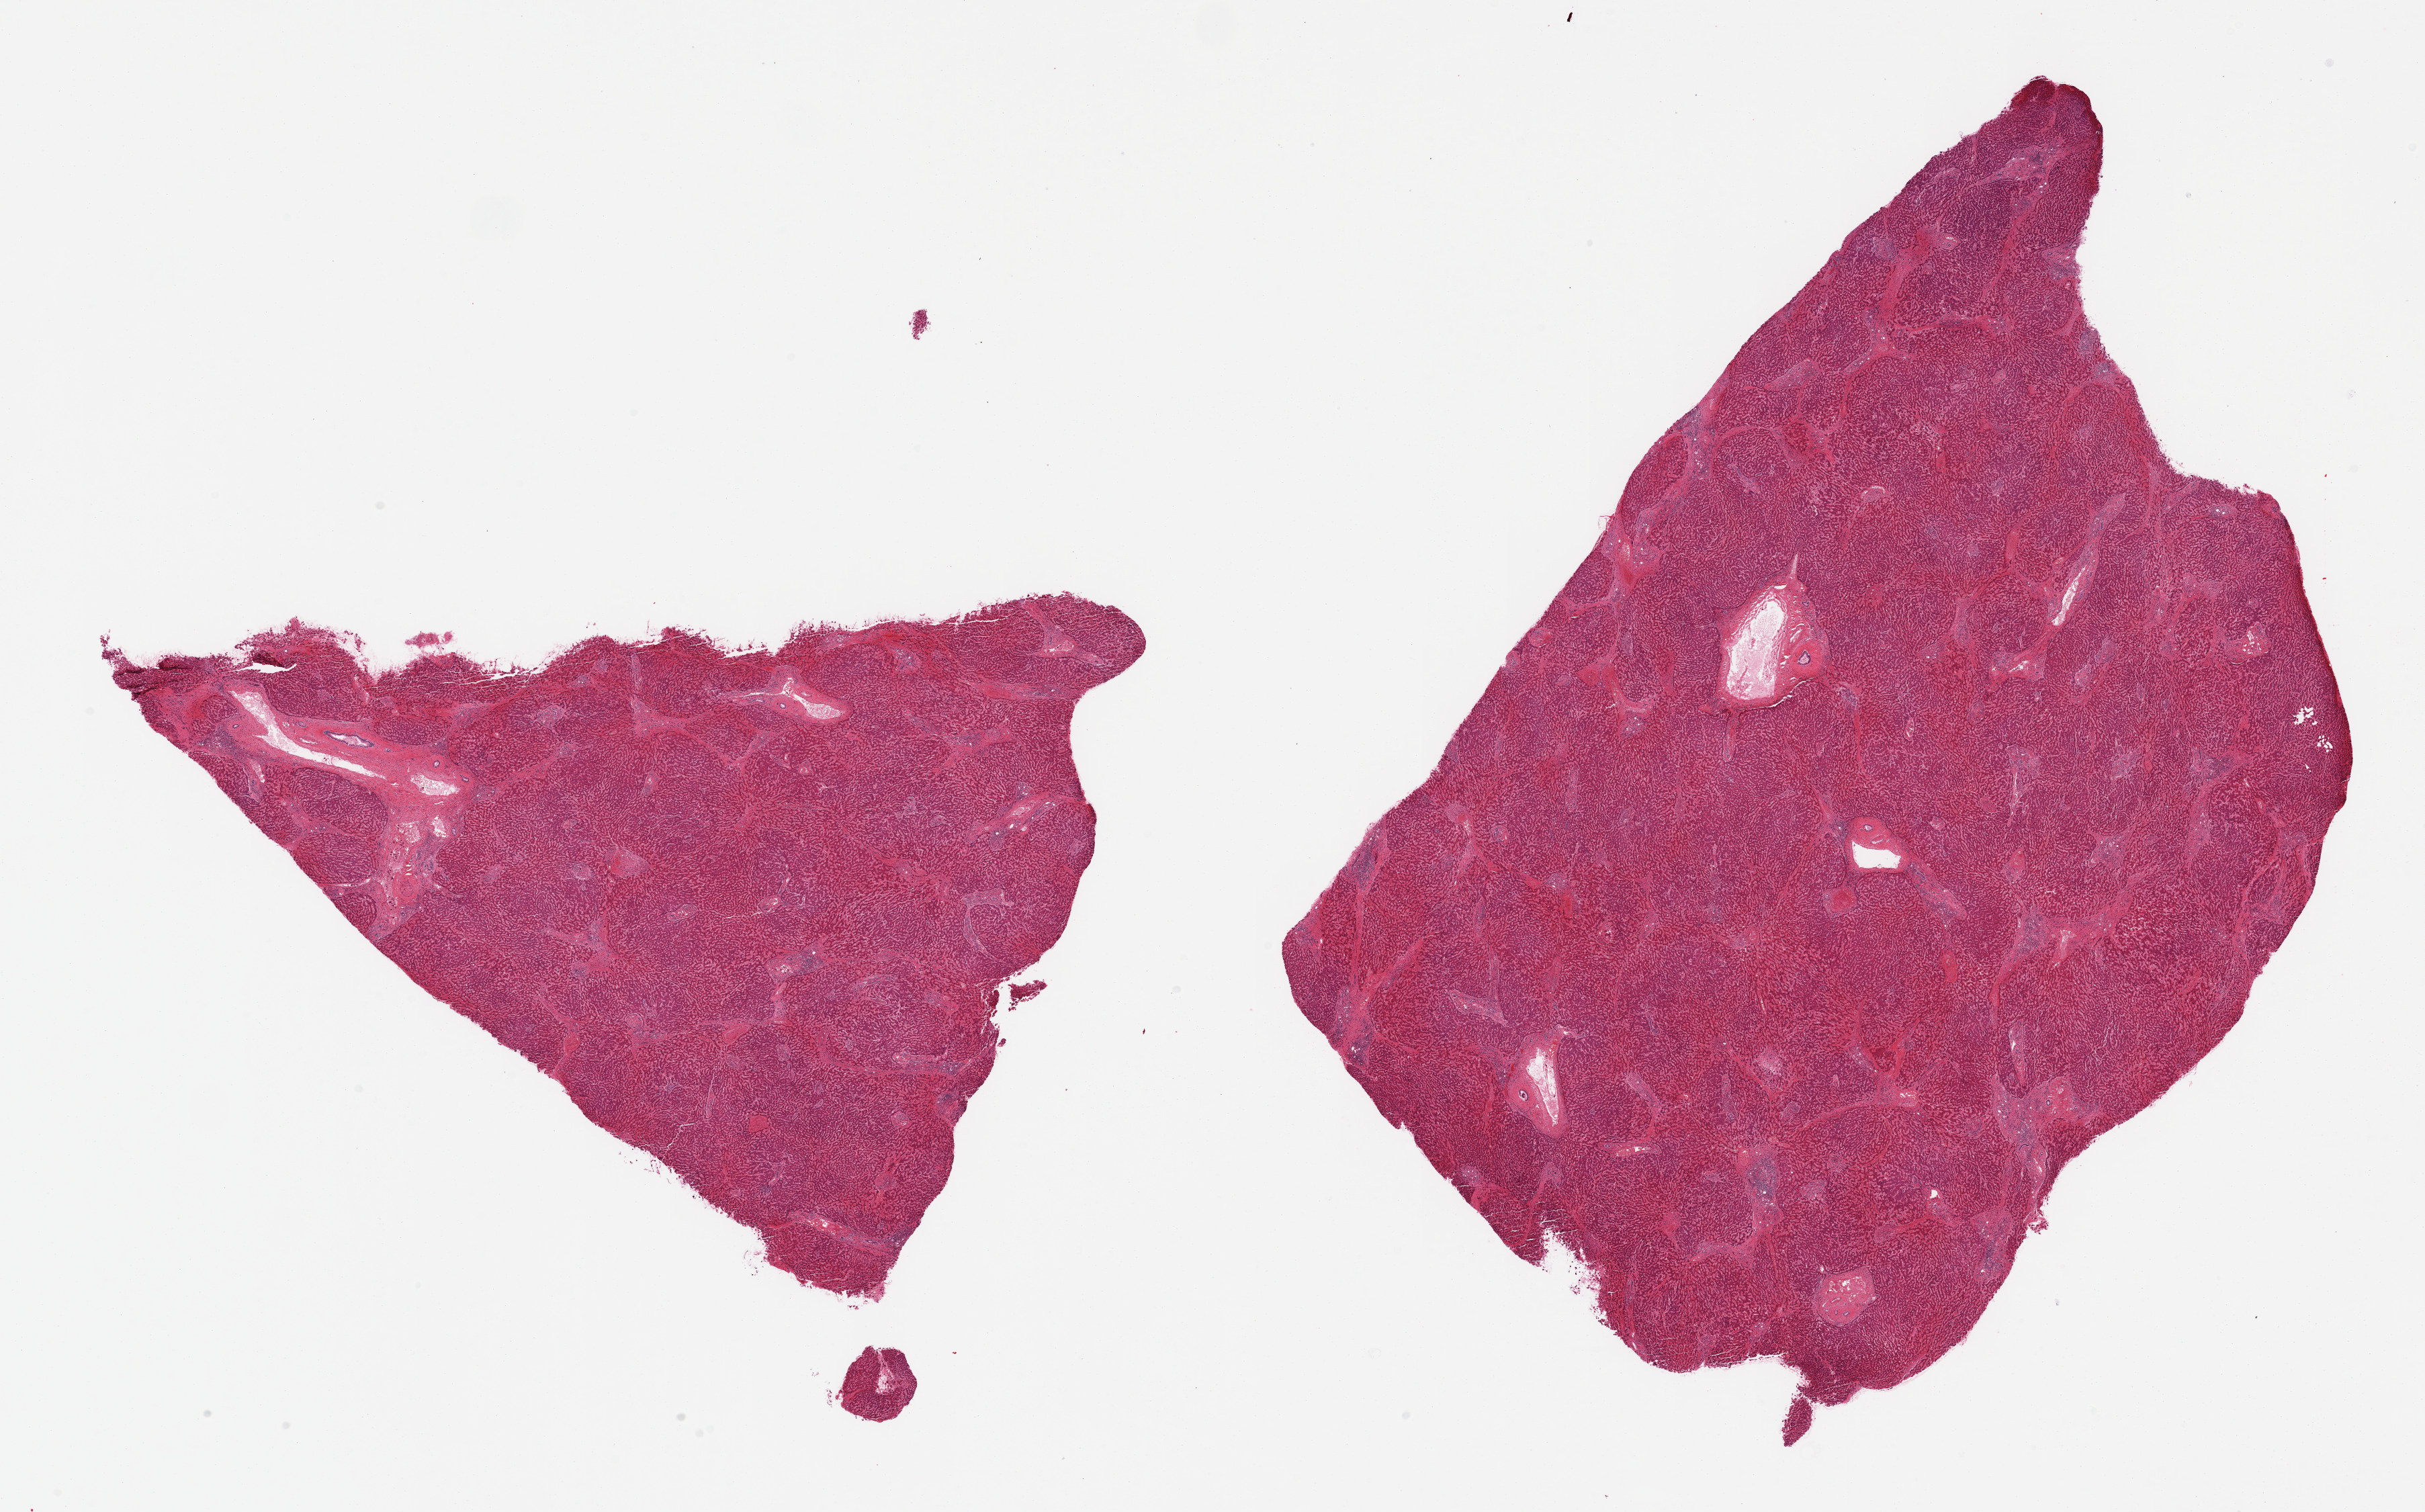
Haematoxylin and eosin whole-slide image, a low-resolution overview of the entire scanned area, about 28.5 x 17.8 mm, PAXgene-fixed, paraffin-embedded tissue, sampled site (target tissue): liver, tissue donor sample. Donor sex: male.
Pathologist's review note for this sample: 2 pieces; expanded portal spaces with lymphocytic increase, fibrous bridging and piecemeal necrosis consistent with low grade chronic hepatitis.